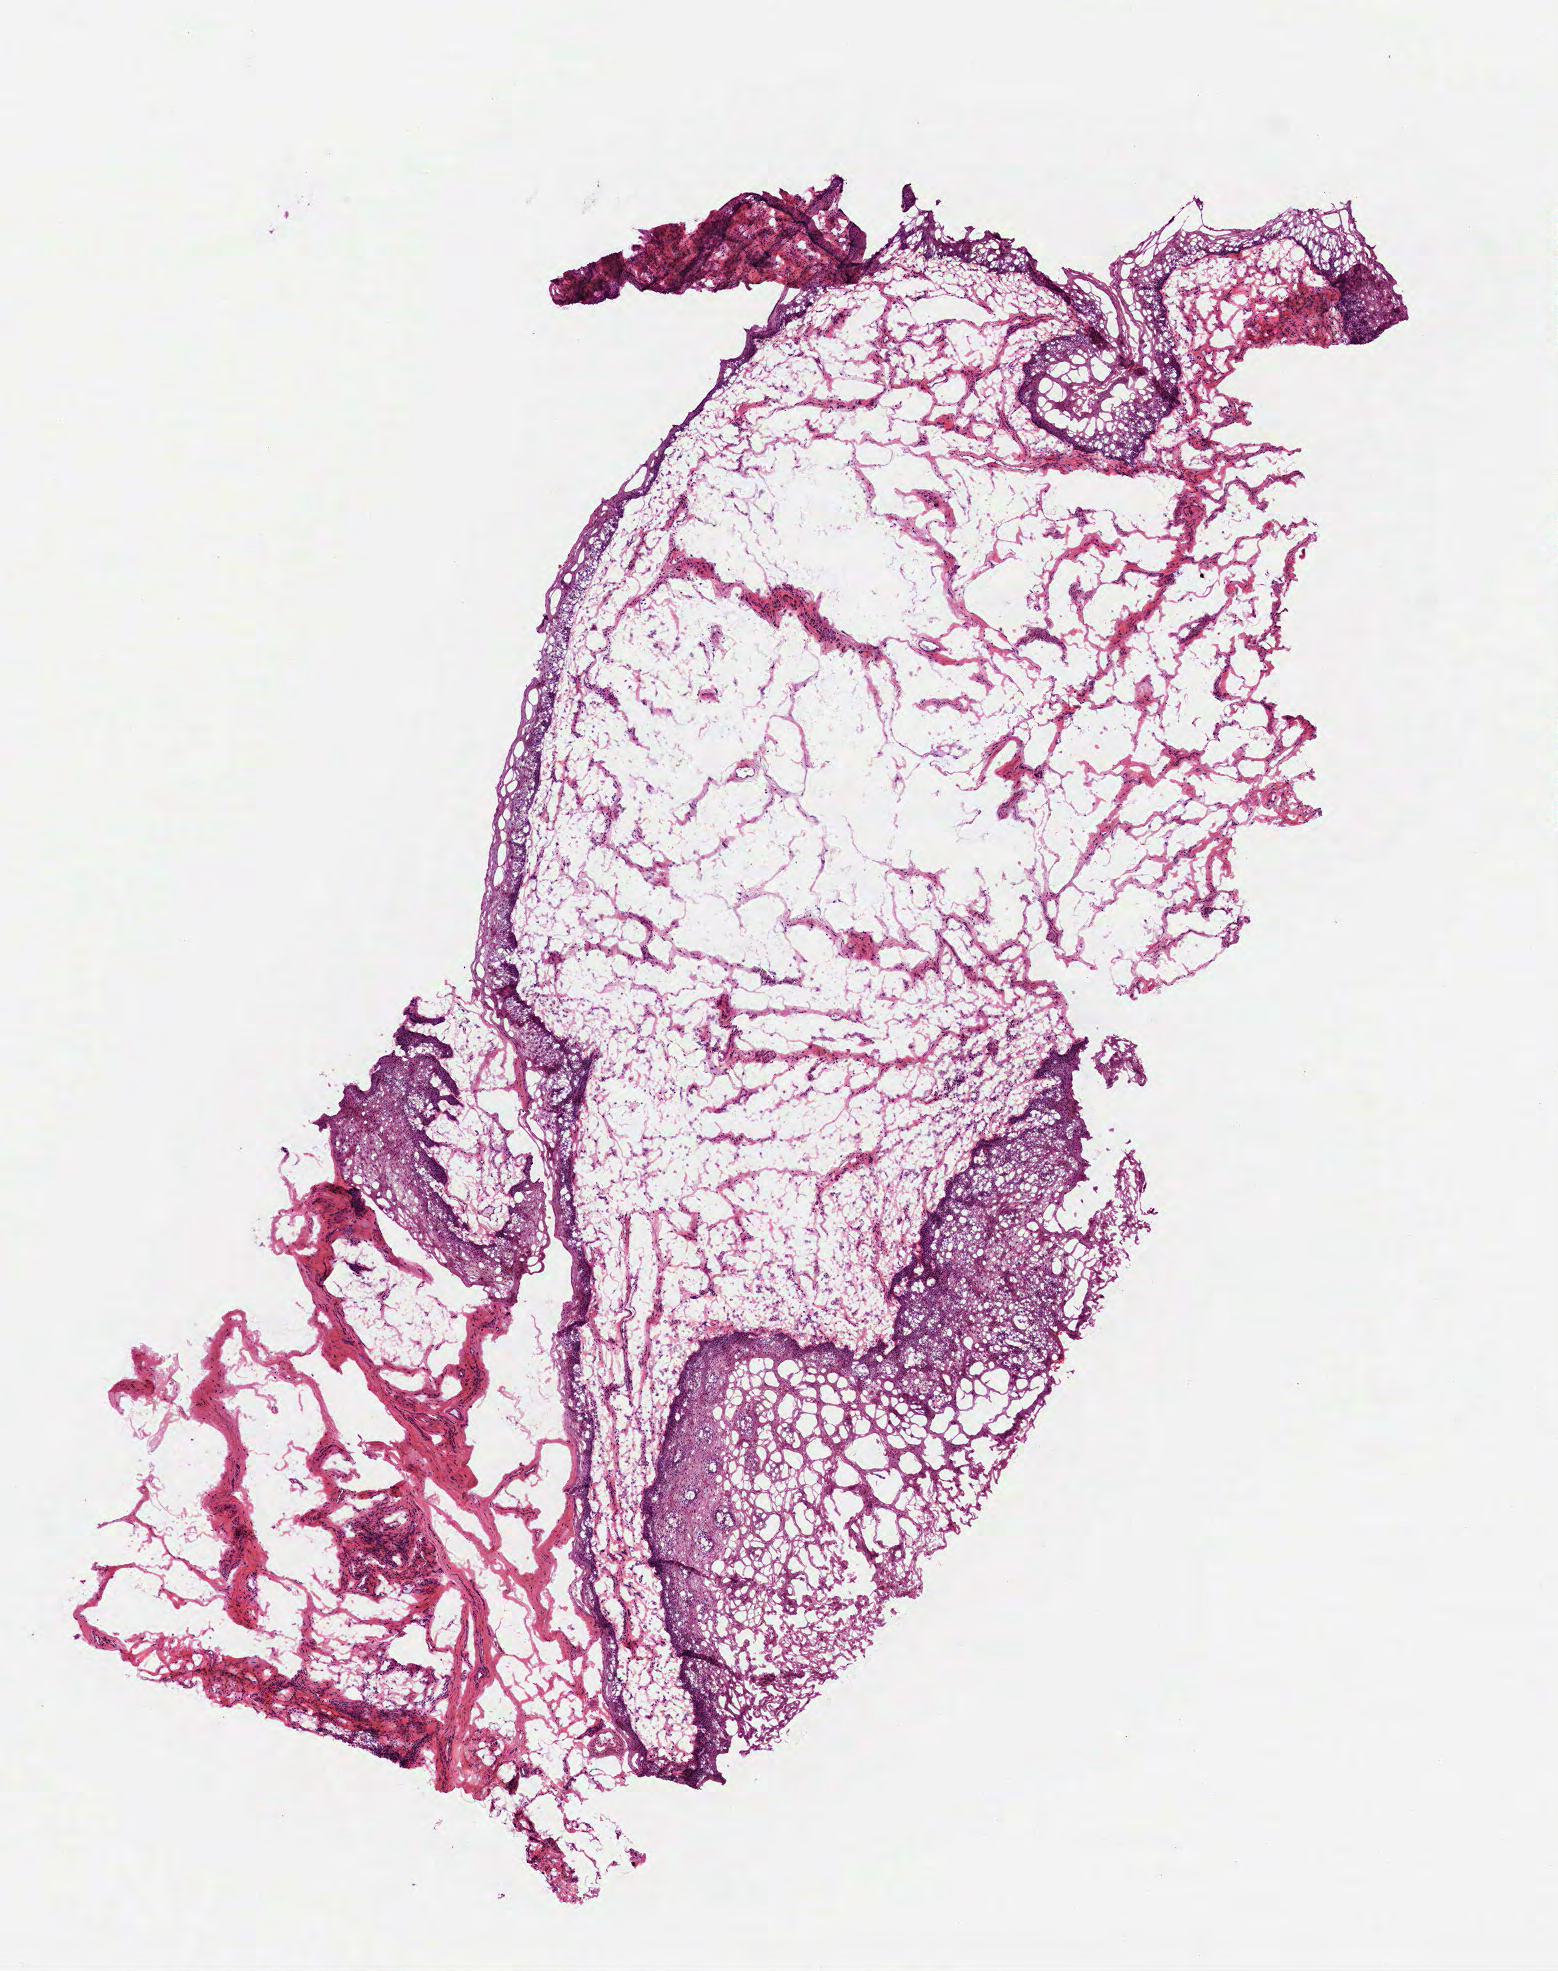
Whole-slide histology image, H&E-stained, shown as a low-resolution overview of the whole scanned area (about 6.3 x 8.0 mm, slide scanned at 40x); frozen section from the top of the tissue portion; sample: solid tissue normal (non-tumour tissue), head and neck. Patient: male, age at initial diagnosis 57 years.
- this section: solid tissue normal sample (biorepository sample class)
- patient diagnosis: Squamous cell carcinoma, NOS